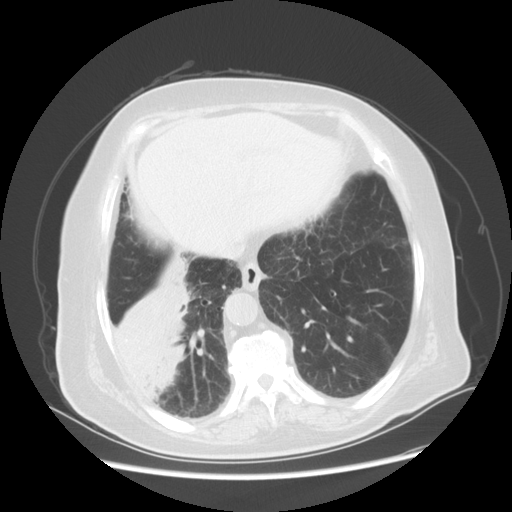
Chest CT, one axial slice. Slice 16 of 56 in the series (ordered by position). Reconstruction kernel STANDARD. 120 kVp. Lung window (W 1500 / L -600 HU). 5 mm slice thickness. 512 × 512 image matrix, field of view 378 × 378 mm. Female patient, age 73 years. From the clinical record (not read from this slice): clinical TNM (as recorded): T3 N0 M0.
Structures marked on this image (rectangle marked by the reading radiologist):
- lung tumour (recorded histology: adenocarcinoma): bounding box <108,258,192,404> (left, top, right, bottom; pixels)